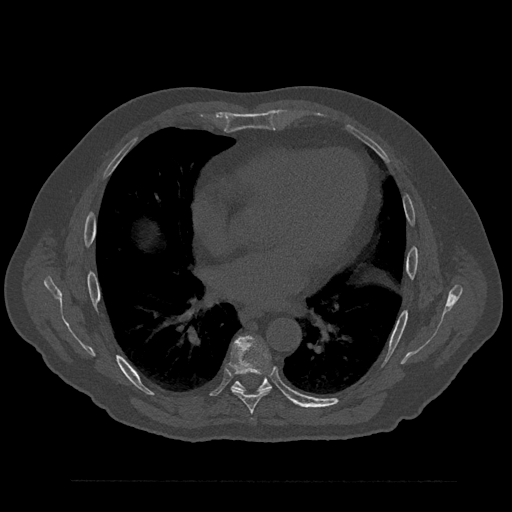
CT including the spine, one axial slice. Bone window (W 1800 / L 400 HU). 0.5 mm slice thickness. 512 × 512 image matrix, field of view 430 × 430 mm. Male patient, age 61 years. From the clinical record (not read from this slice): primary cancer: prostate.
Annotated regions visible in this slice (semi-automatically segmented with operator editing):
- T7 vertebra: bounding box [x1, y1, x2, y2] px = [229, 336, 272, 414]
- T8 vertebra: [232, 377, 272, 392]